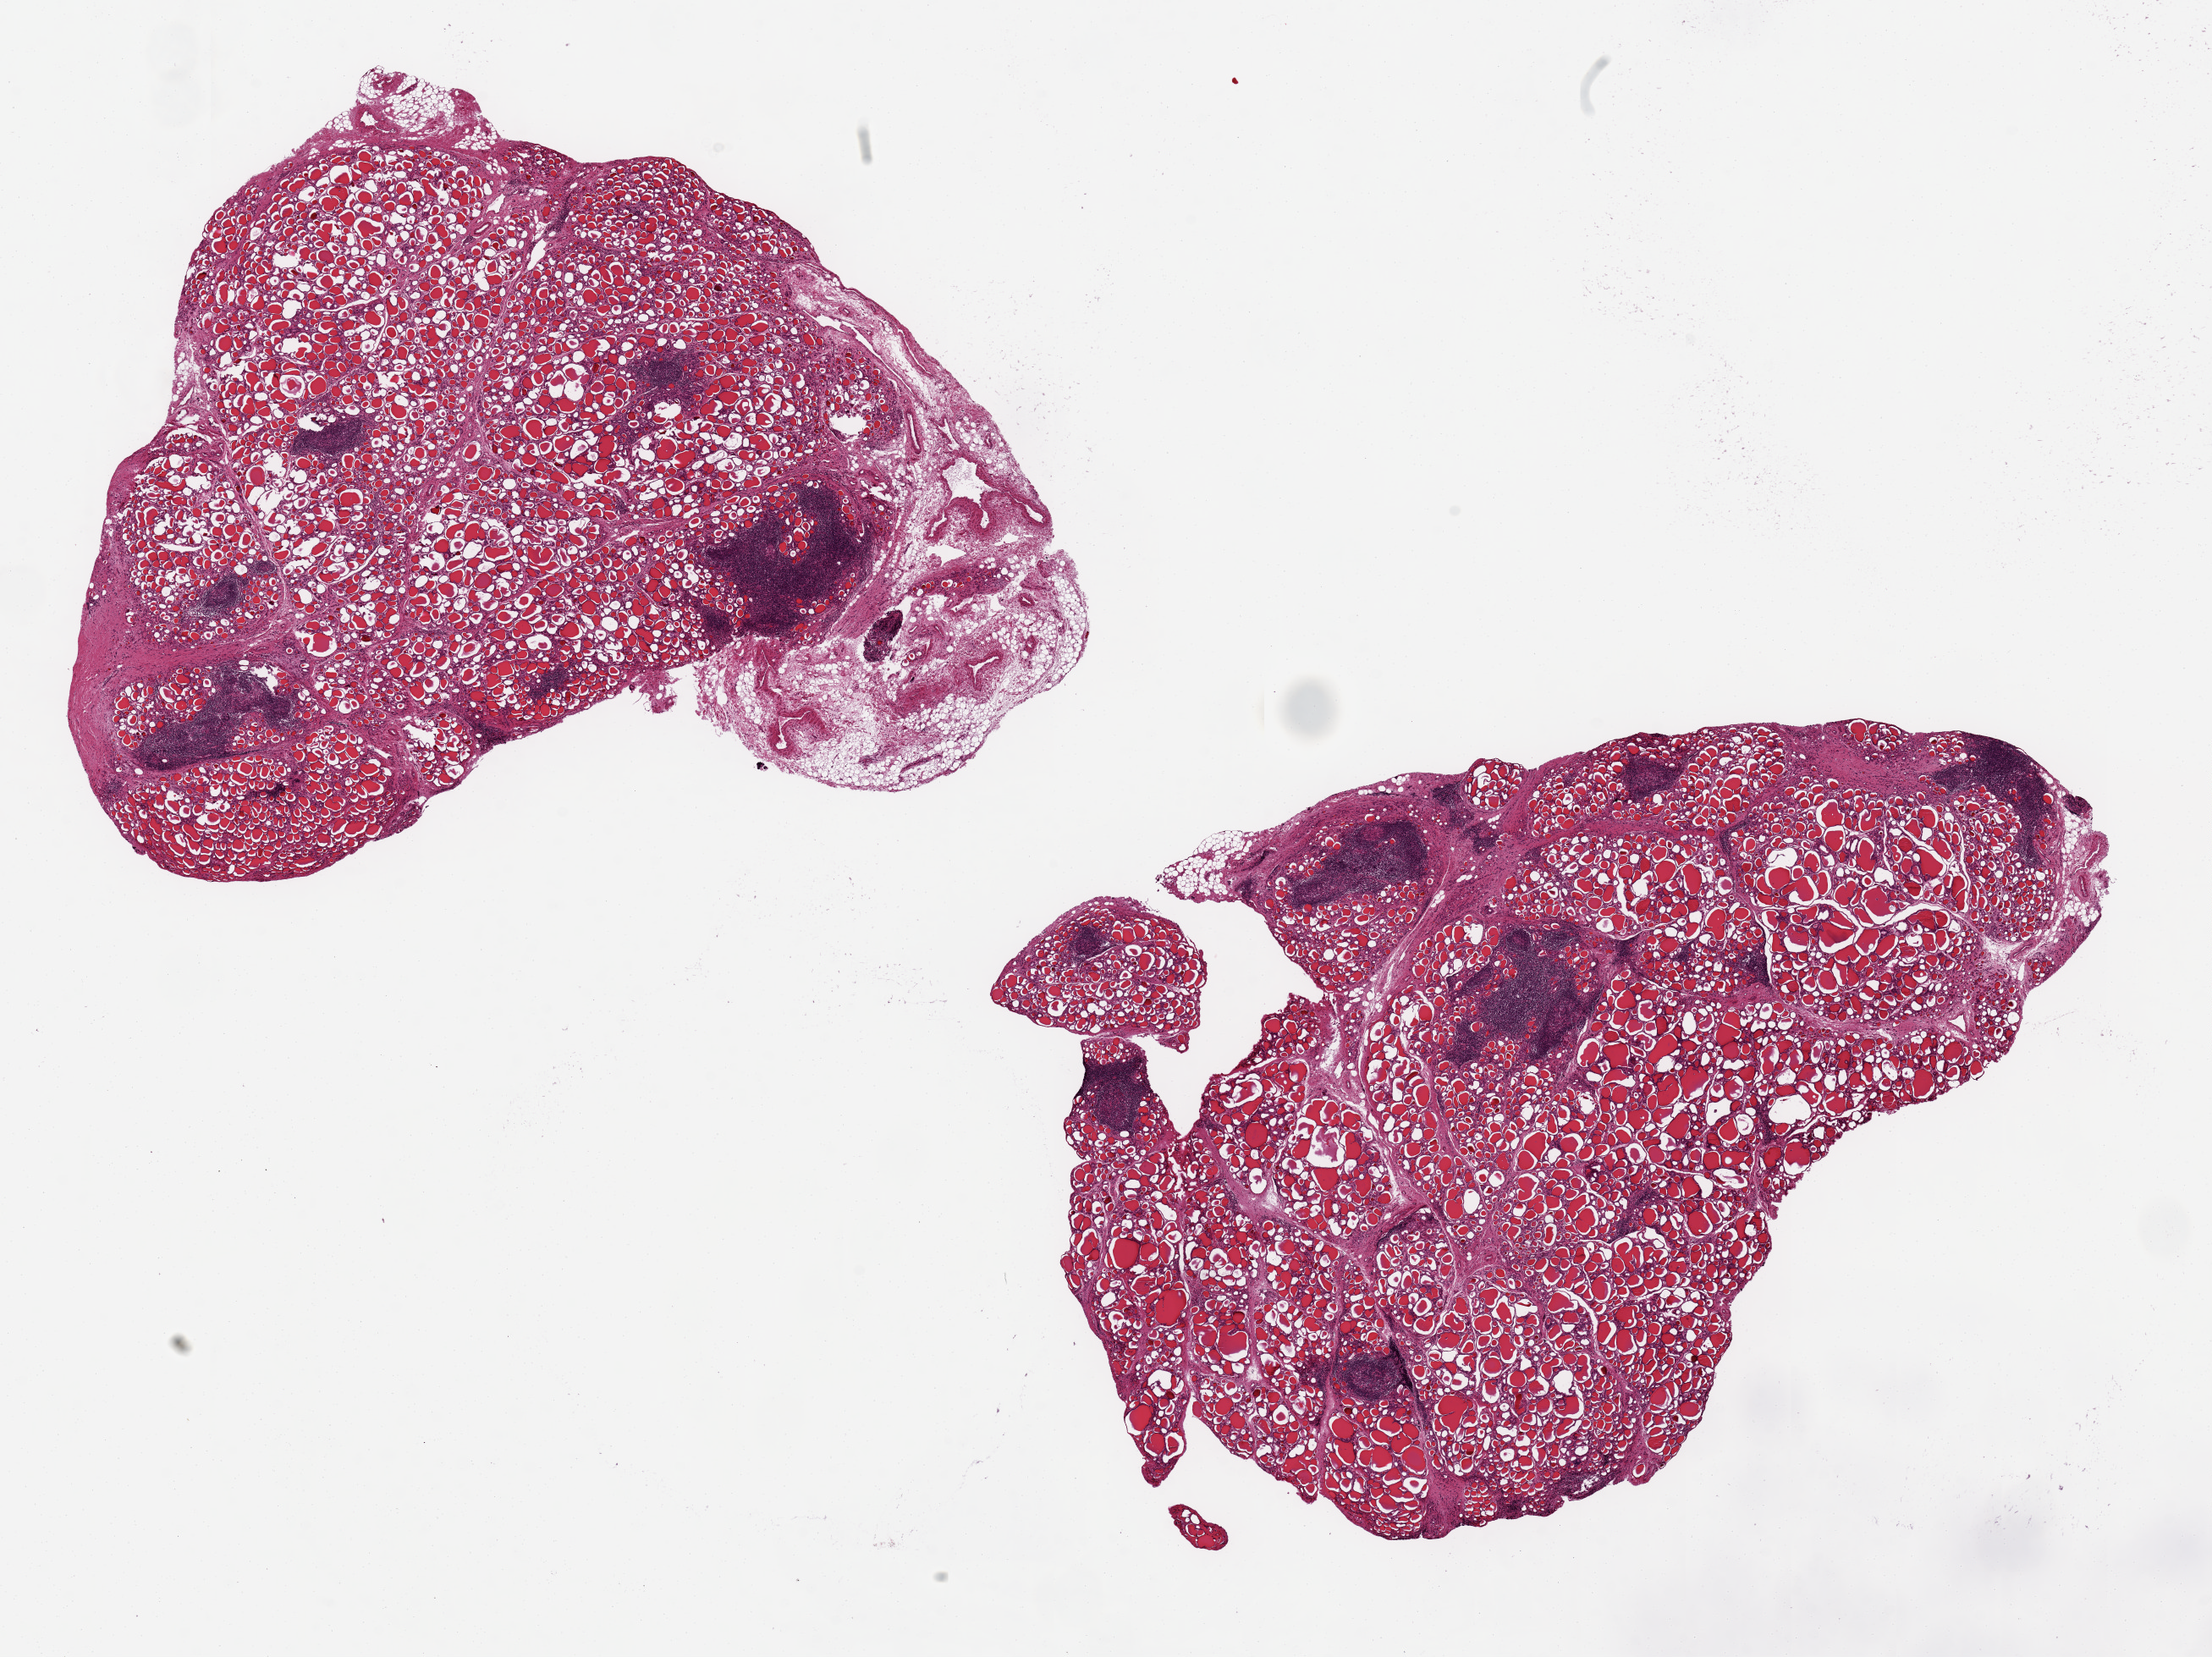
Digitized hematoxylin and eosin (H&E)-stained section — a low-resolution overview of the entire scanned area, about 20.7 x 15.5 mm (slide scanned at 20x). PAXgene-fixed paraffin-embedded (PFPE) section. Sampled site (target tissue): thyroid. Tissue donor sample. Donor: female.
Review note (as recorded): 2 aliquots, ~9x7mm. Patchy, diffuse lymphocytic/Hashimoto thyroiditis.